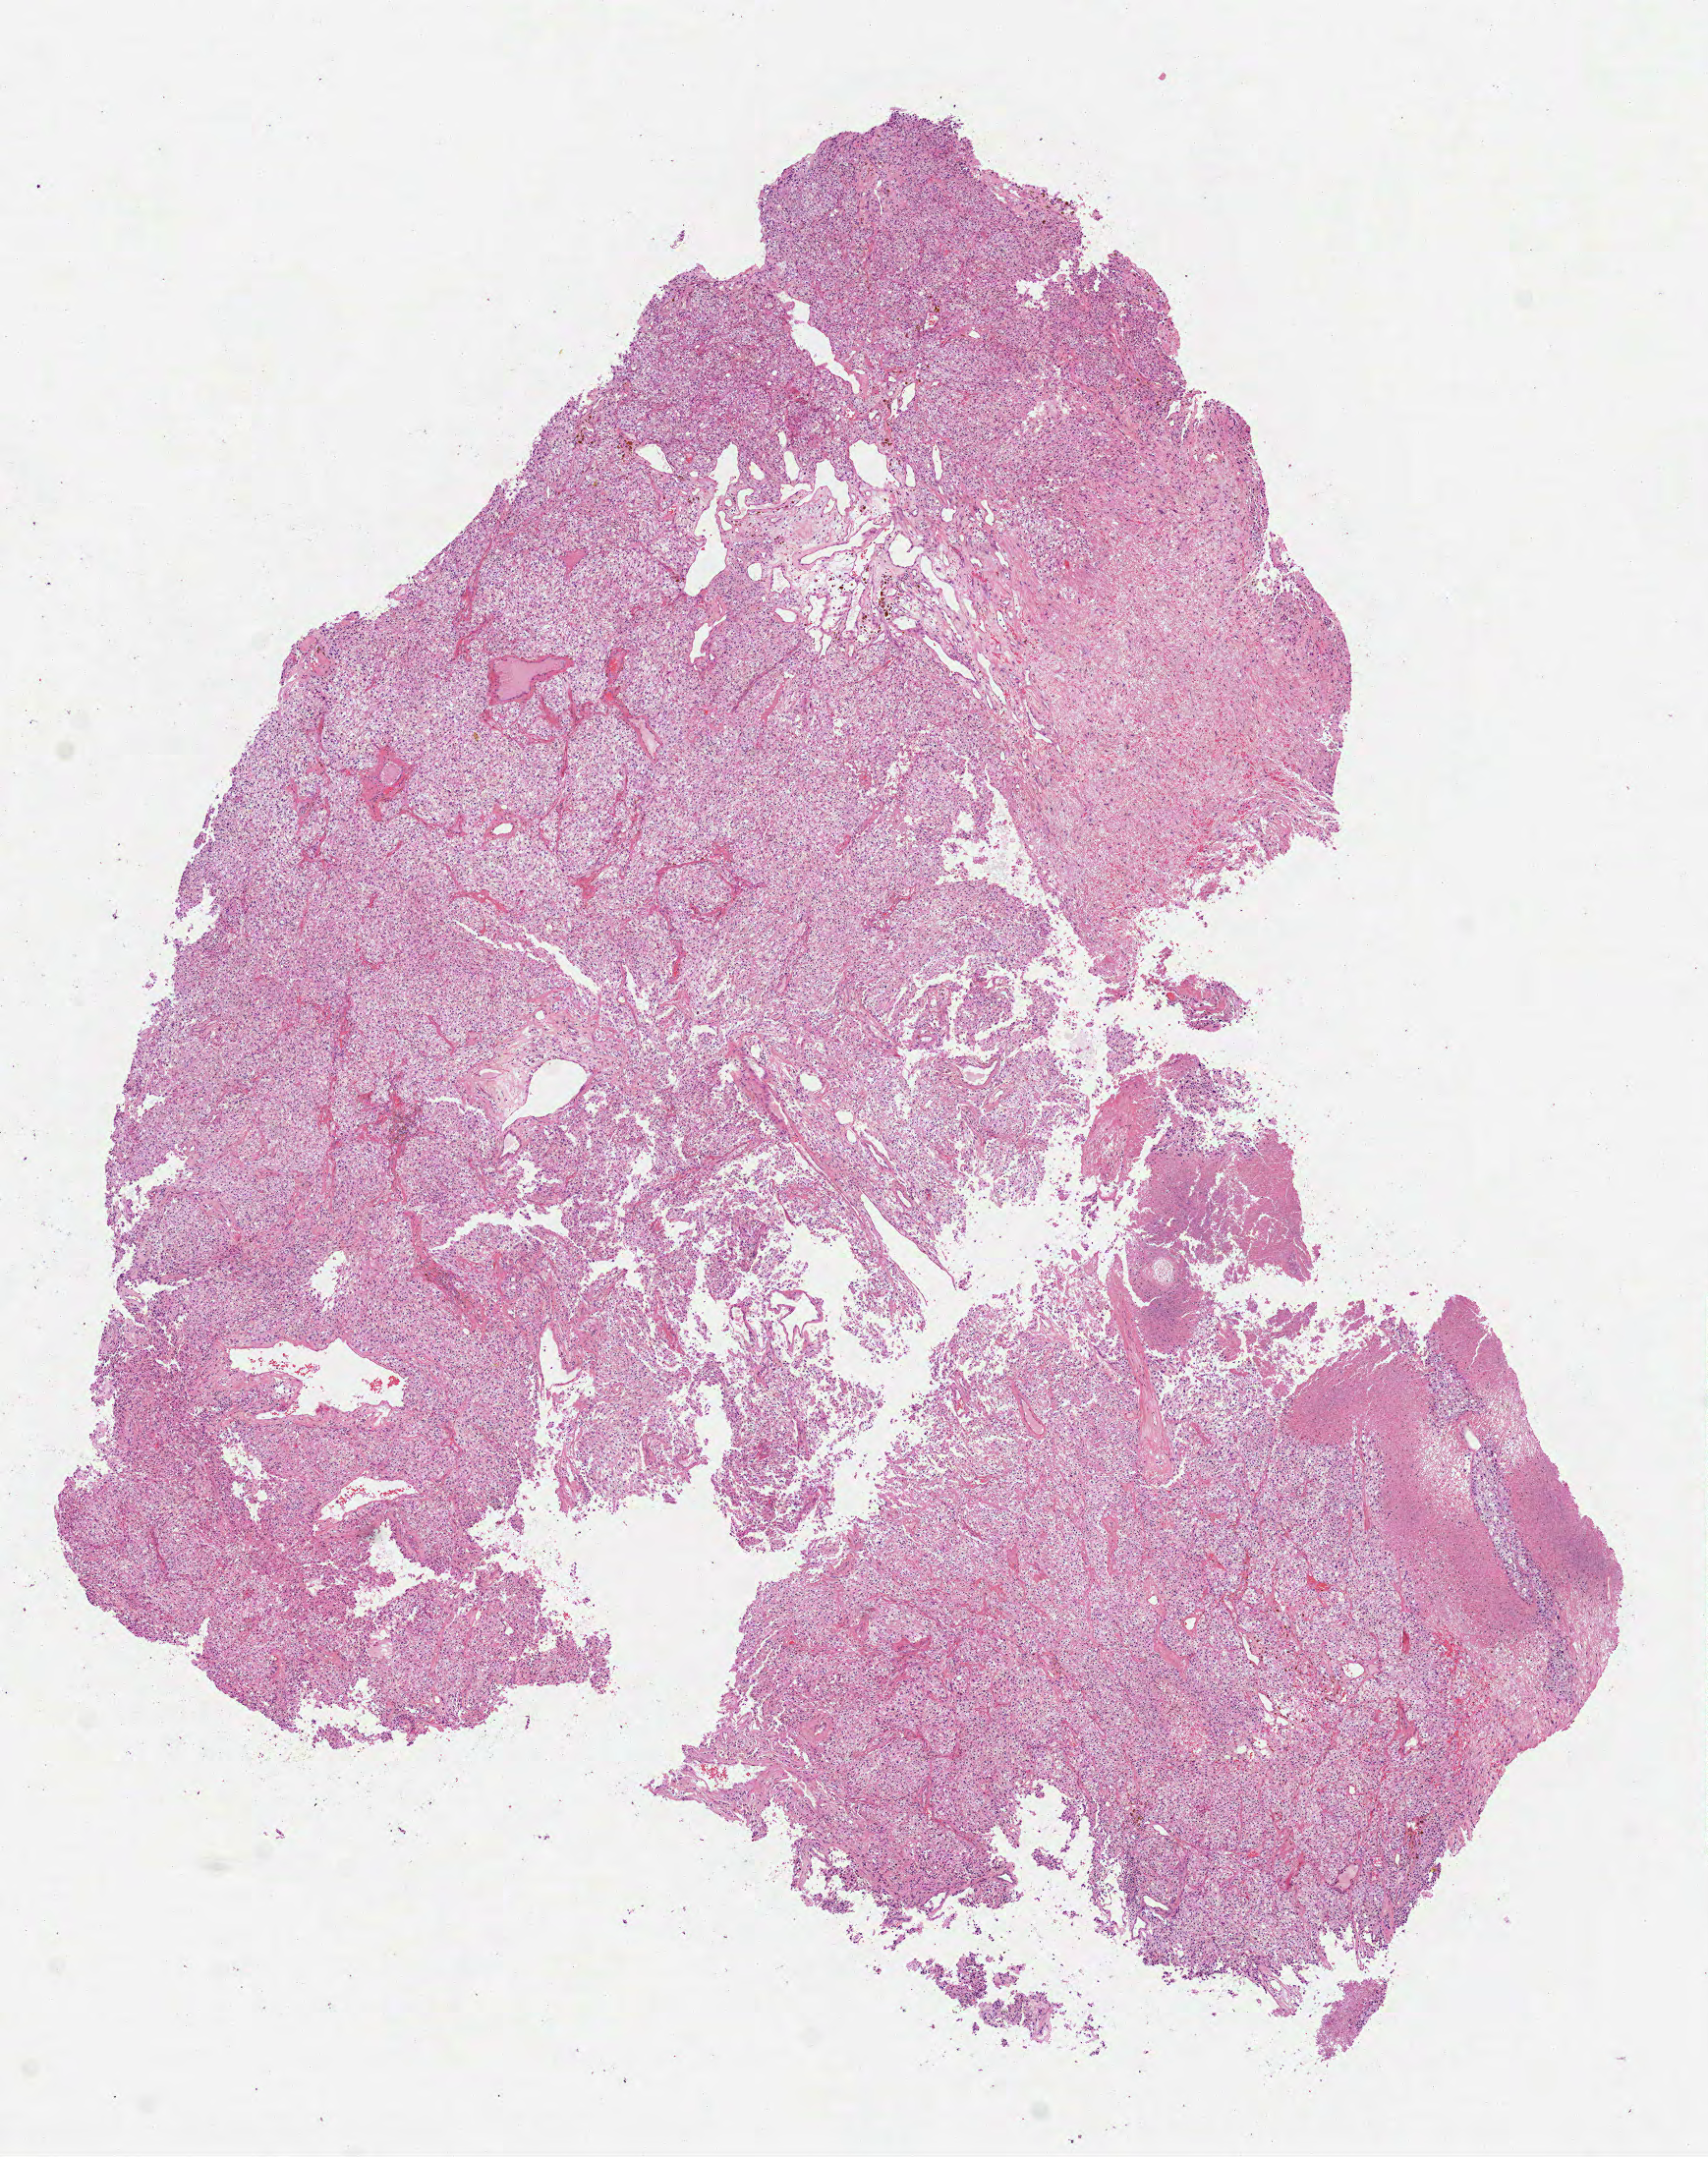
Whole-slide histology image, H&E, a low-resolution overview of the entire scanned area, about 7.0 x 8.9 mm (acquisition: 40x scan). FFPE section. Sample: primary tumour, kidney. Male patient; age at initial diagnosis 68 years. Histologic grade: G3 (poorly differentiated).
AJCC pathologic stage: I. Pathologic diagnosis: Clear cell adenocarcinoma, NOS. TNM: T1b NX M0.